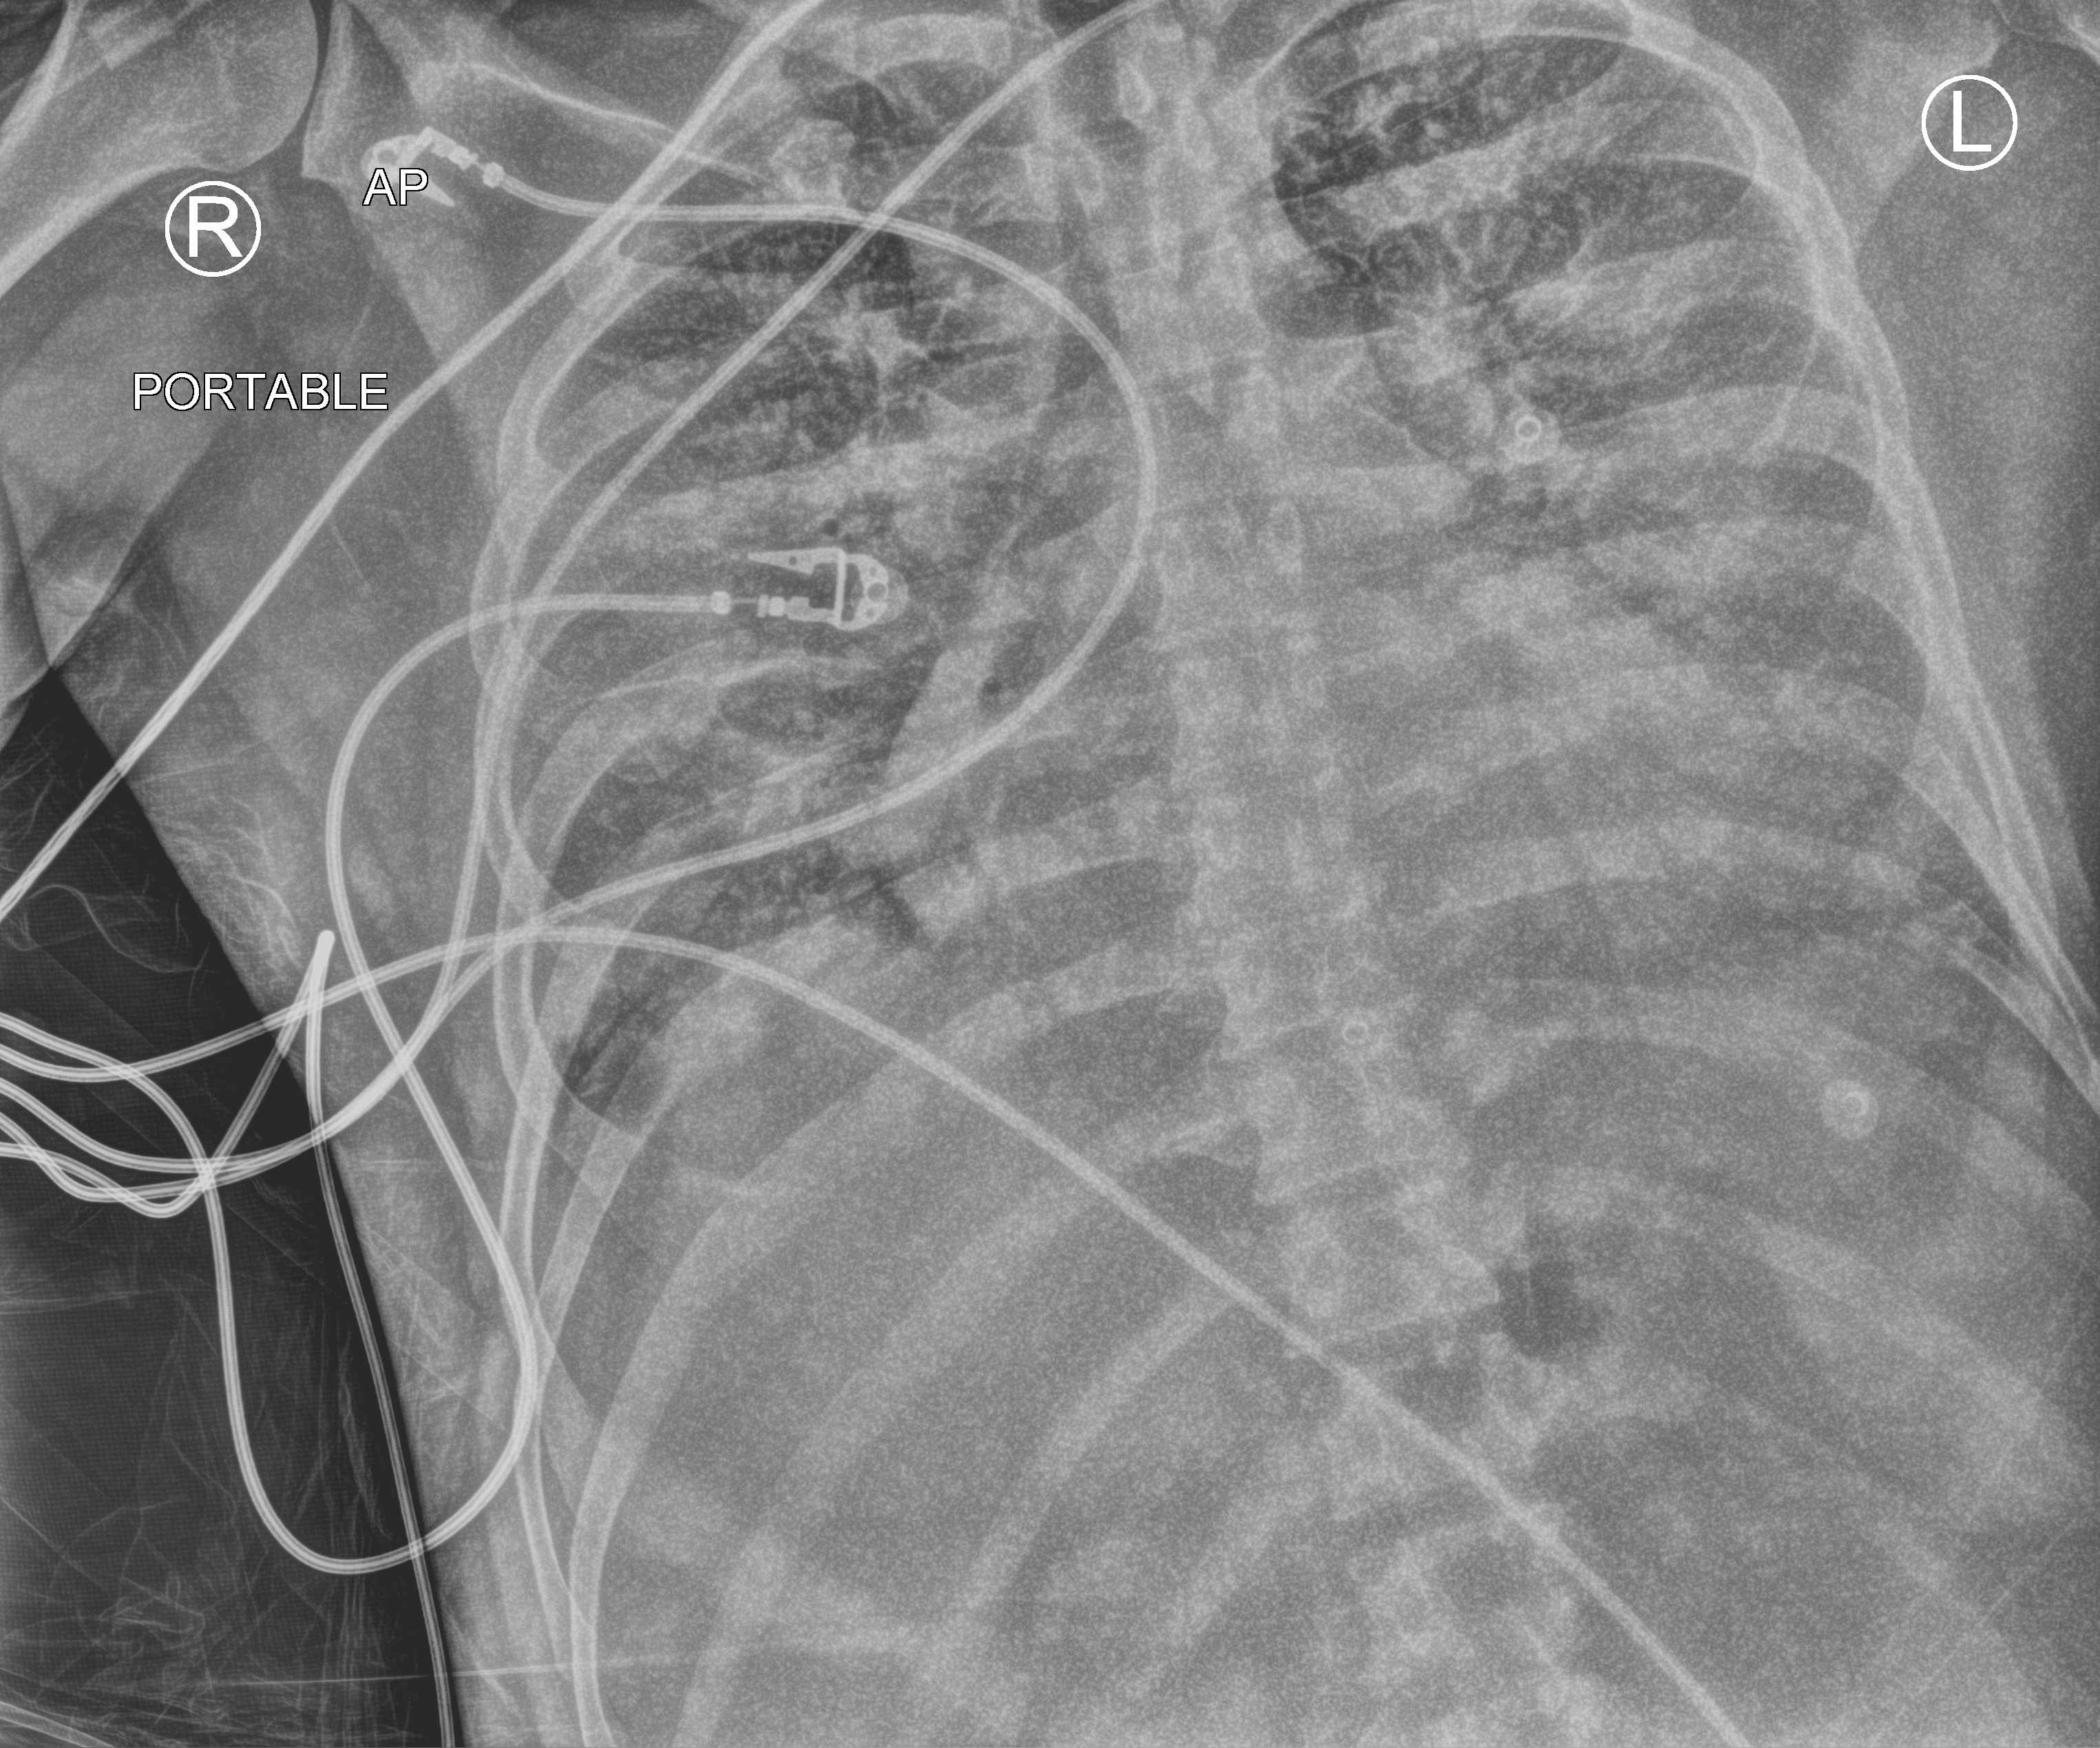
Portable chest radiograph, anteroposterior (AP) projection. Patient hospitalised with COVID-19; male, aged 18–59 years.
From the hospital-stay record, not from the radiograph (when in the stay this image was taken is not recorded): diabetes (admission record): no; mechanically ventilated during this hospital stay: yes; admitted to intensive care during this hospital stay: yes.